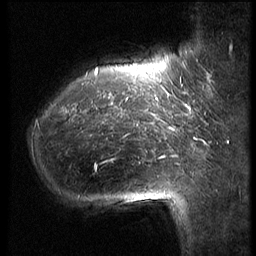
Breast MRI (dynamic contrast-enhanced), one sagittal slice. Position 12 of 62 along the scan axis. 3 images stored at this slice position (order not interpretable as contrast timing). 1.5 T. TE 4.2 ms, TR 9 ms. 2.5 mm slice thickness. 256 × 256 image matrix. Female patient, age 39 years. Case-level facts recorded for this patient, not image findings: setting: breast cancer imaged before/during neoadjuvant chemotherapy; receptor status: HER2-positive.
Outlined on this slice (semi-automatically segmented with operator editing):
- analysis volume of interest (the breast-tissue region the enhancement analysis was run in; not a lesion): bounding box <29,64,171,226> (left, top, right, bottom; pixels)
- tumour enhancement mask (voxels above the 140 % enhancement threshold inside the analysis volume of interest): <95,67,171,162>